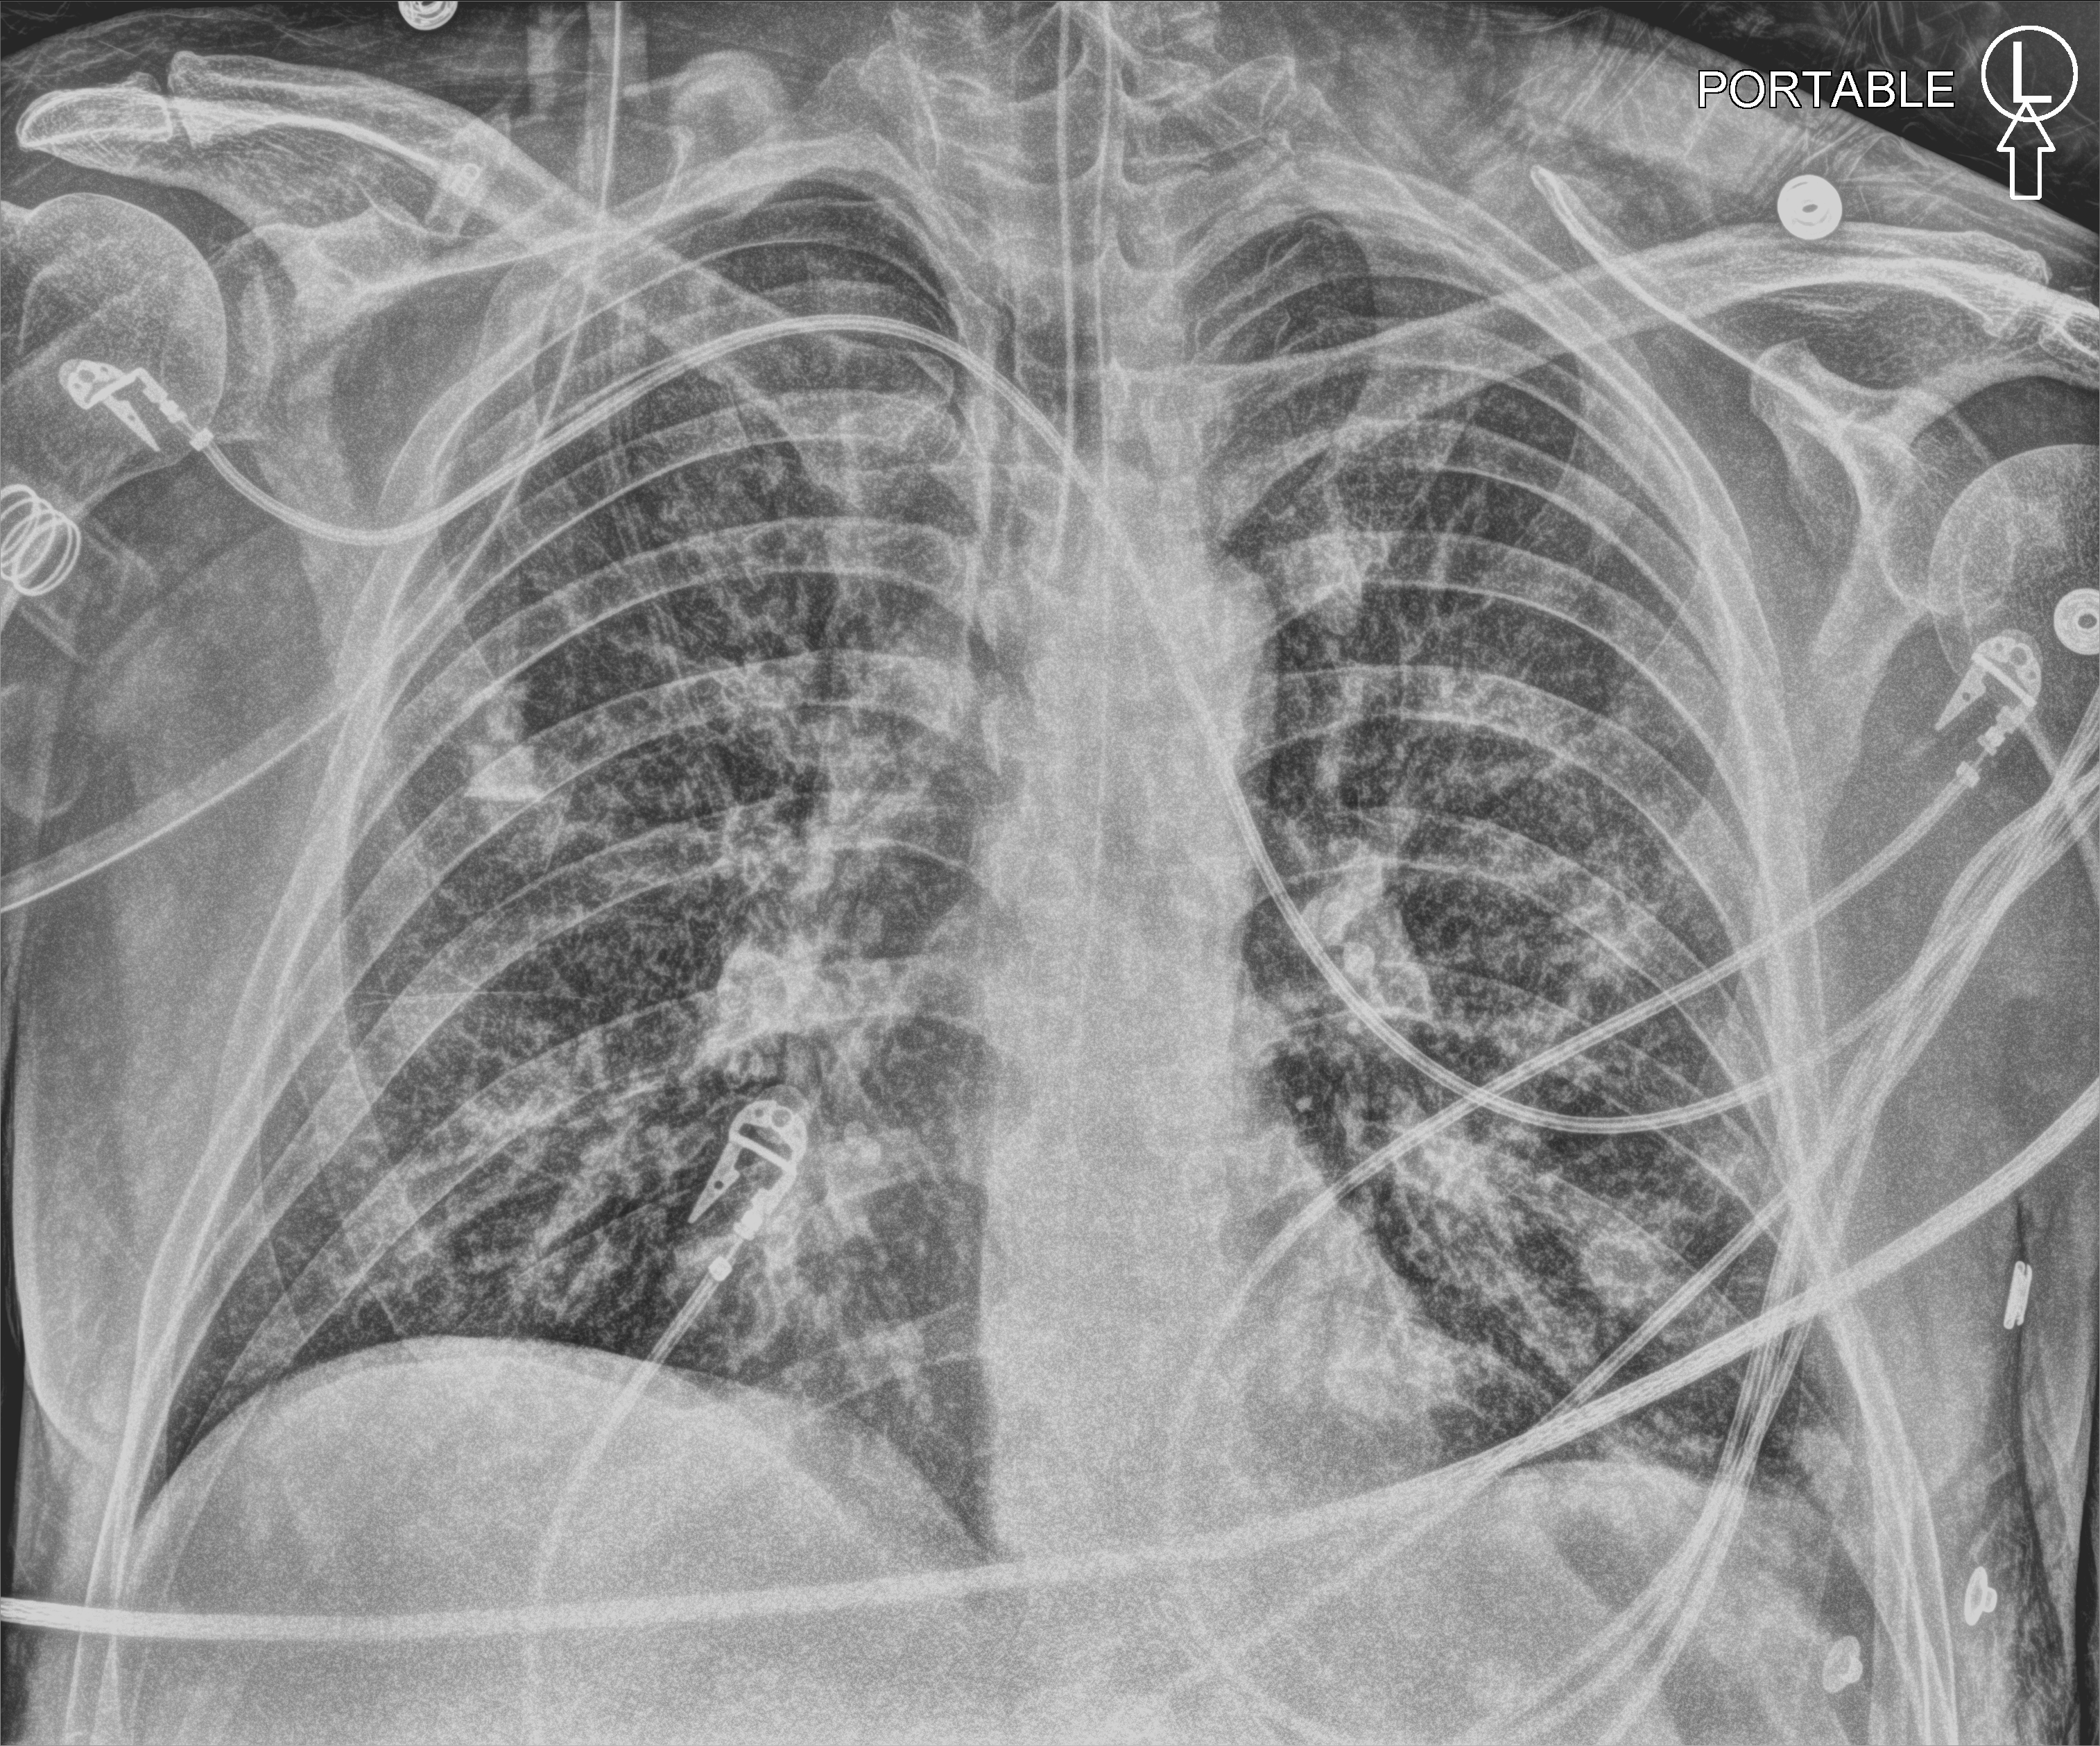
Chest X-ray (portable), anteroposterior (AP) projection. Patient hospitalised with COVID-19; male, aged 18–59 years.
Hospital-stay facts (about this admission, not read from this image; timing relative to this image not recorded):
- mechanically ventilated during this hospital stay: yes
- admitted to intensive care during this hospital stay: no
- other chronic lung disease (admission record): no